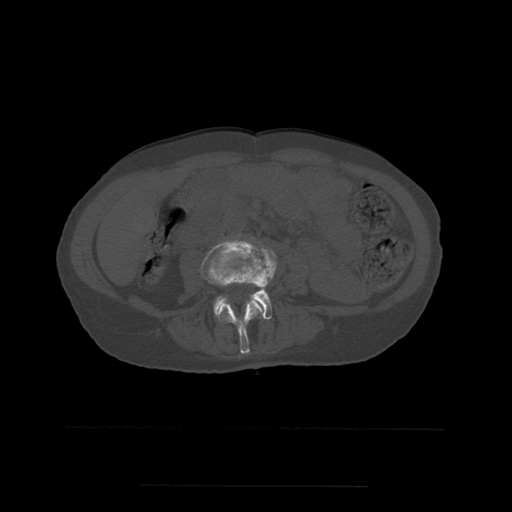
CT including the spine, one axial slice. Slice 179 of 544 in the series (ordered by position). Bone window (W 1800 / L 400 HU). 1.25 mm slice thickness. 512 × 512 image matrix, field of view 350 × 350 mm. Patient age 58 years. From the clinical record (not read from this slice): primary cancer: lung.
Outlined on this slice (semi-automatic segmentation, software-assisted and operator-edited):
- L1 vertebra: bounding box (x1, y1, x2, y2) in pixels: (218, 270, 259, 318)
- L3 vertebra: (201, 240, 273, 354)
- L4 vertebra: (214, 249, 277, 320)